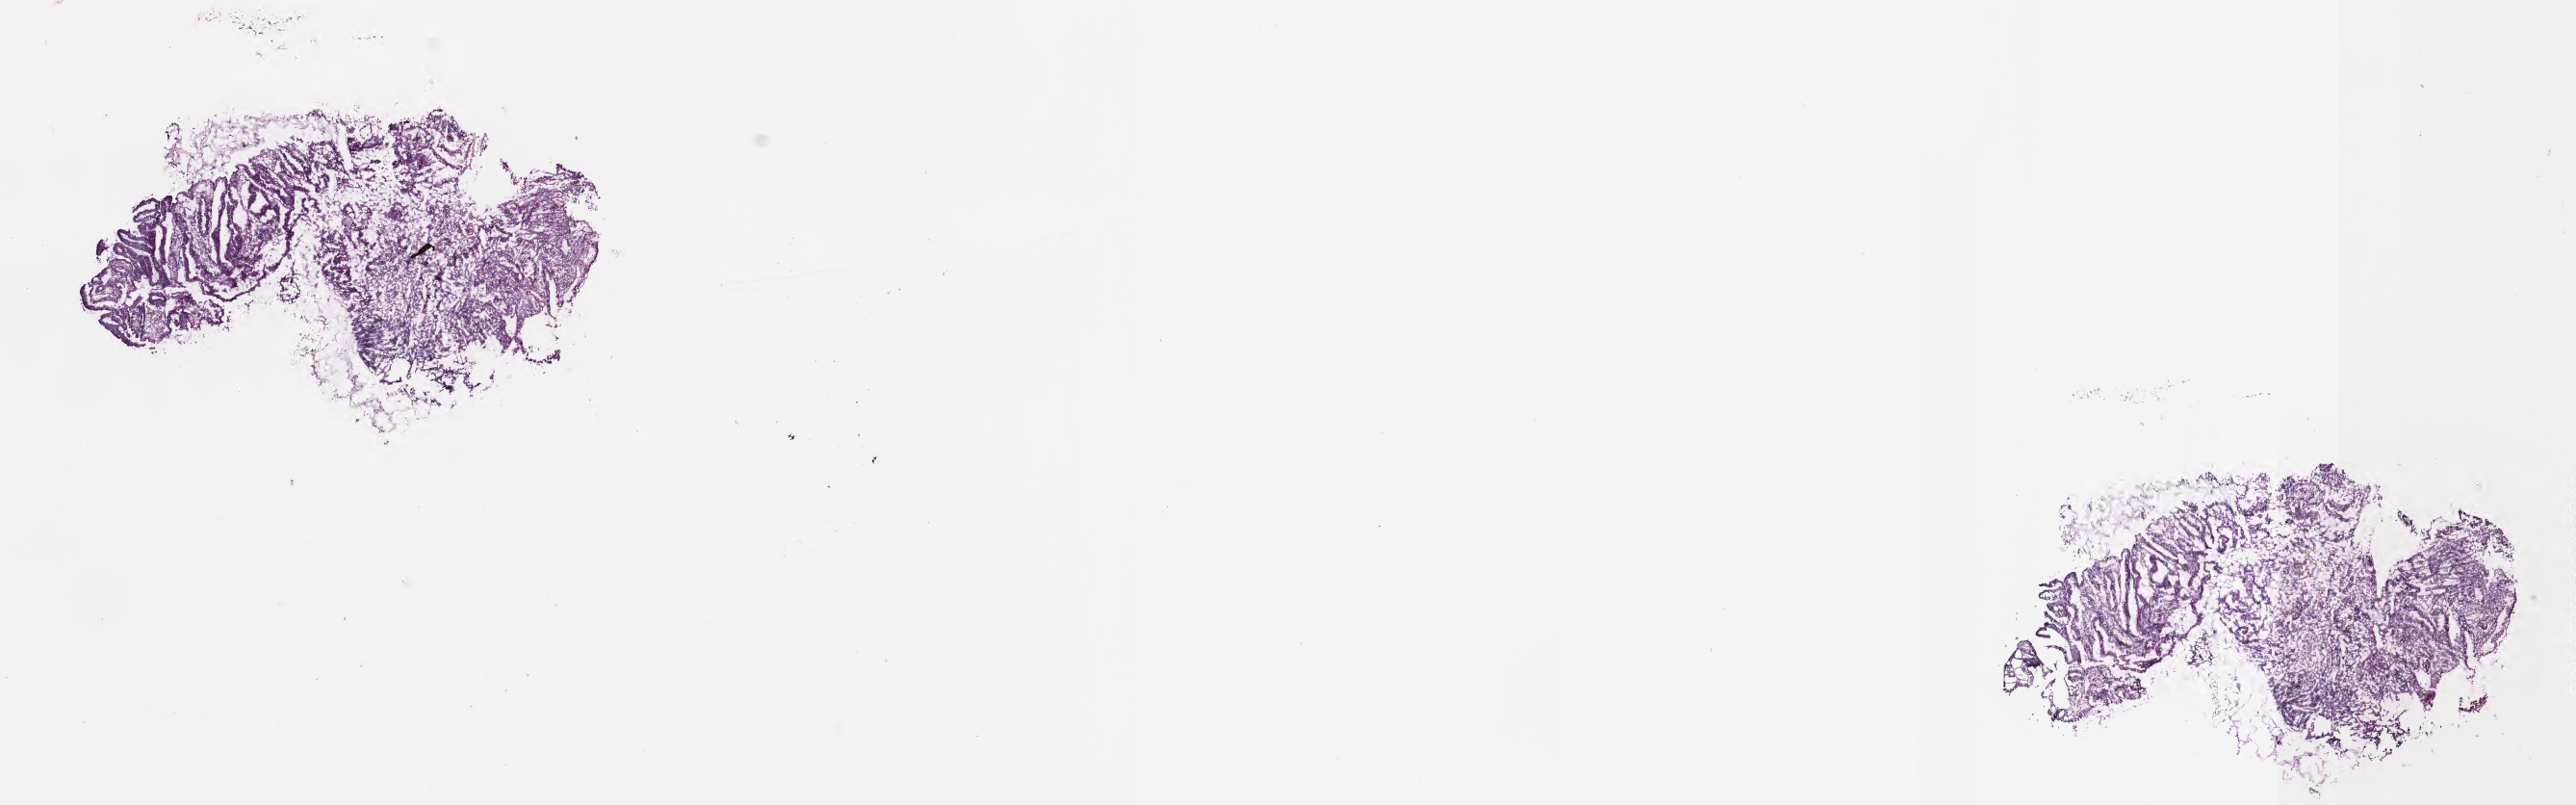
Whole-slide image, haematoxylin and eosin stain — shown as a low-resolution overview of the whole scanned area (about 21.6 x 6.8 mm); cryosection; specimen: primary tumor; anatomic site: ascending colon. Patient: female, age at initial diagnosis 60 years. Tumor grade: GB (borderline). Slide review estimates, as recorded: tumor cells 40%, tumor nuclei 40%, stromal cells 40%, necrosis 0%, normal cells 20%. Inflammatory infiltration, as recorded: lymphocyte infiltration 10%, monocyte infiltration 2%, neutrophil infiltration 5%.
- histologic diagnosis: Adenocarcinoma, NOS
- AJCC pathologic stage: Stage IIIA